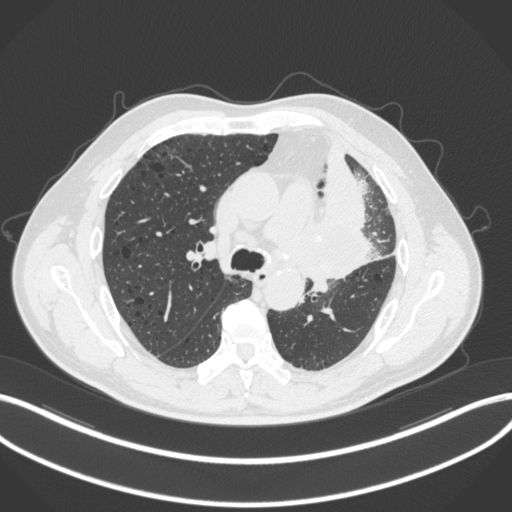
Chest CT, one axial slice; position 185 of 286 along the scan axis; 120 kVp; lung window (W 1500 / L -600 HU); 1 mm slice thickness; 512 × 512 image matrix, field of view 400 × 400 mm. Male patient, age 68 years. From the clinical record (not read from this slice): clinical TNM (as recorded): T3 N3 M1.
Annotated regions visible in this slice (rectangle marked by the reading radiologist):
- lung tumour (recorded histology: adenocarcinoma): box from (x=305, y=188) to (x=387, y=286) px